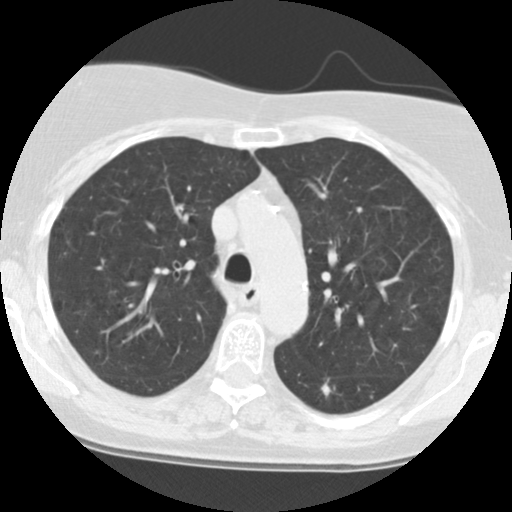
Axial slice from a low-dose chest CT screening exam. Baseline annual screen. Lung window (W 1500 / L -600 HU). 2.5 mm slice thickness. 120 kVp. Female participant, aged 63 years at enrolment. Current smoker at enrolment.
Expert-annotated lung lesion, box from (x=301, y=369) to (x=350, y=410) px. The screening reader recorded 2 non-calcified nodules or masses ≥4 mm on this exam; which of them this box marks is not recorded. Official screen result: positive, change unspecified: nodule(s) >= 4 mm or enlarging nodule(s), mass(es), or other non-specific abnormalities suspicious for lung cancer. Participant outcome: lung cancer diagnosed 796 days after this screen — squamous cell carcinoma, NOS, left lower lobe, moderately differentiated (G2), stage IB (AJCC 6th edition), 15 mm at pathology.